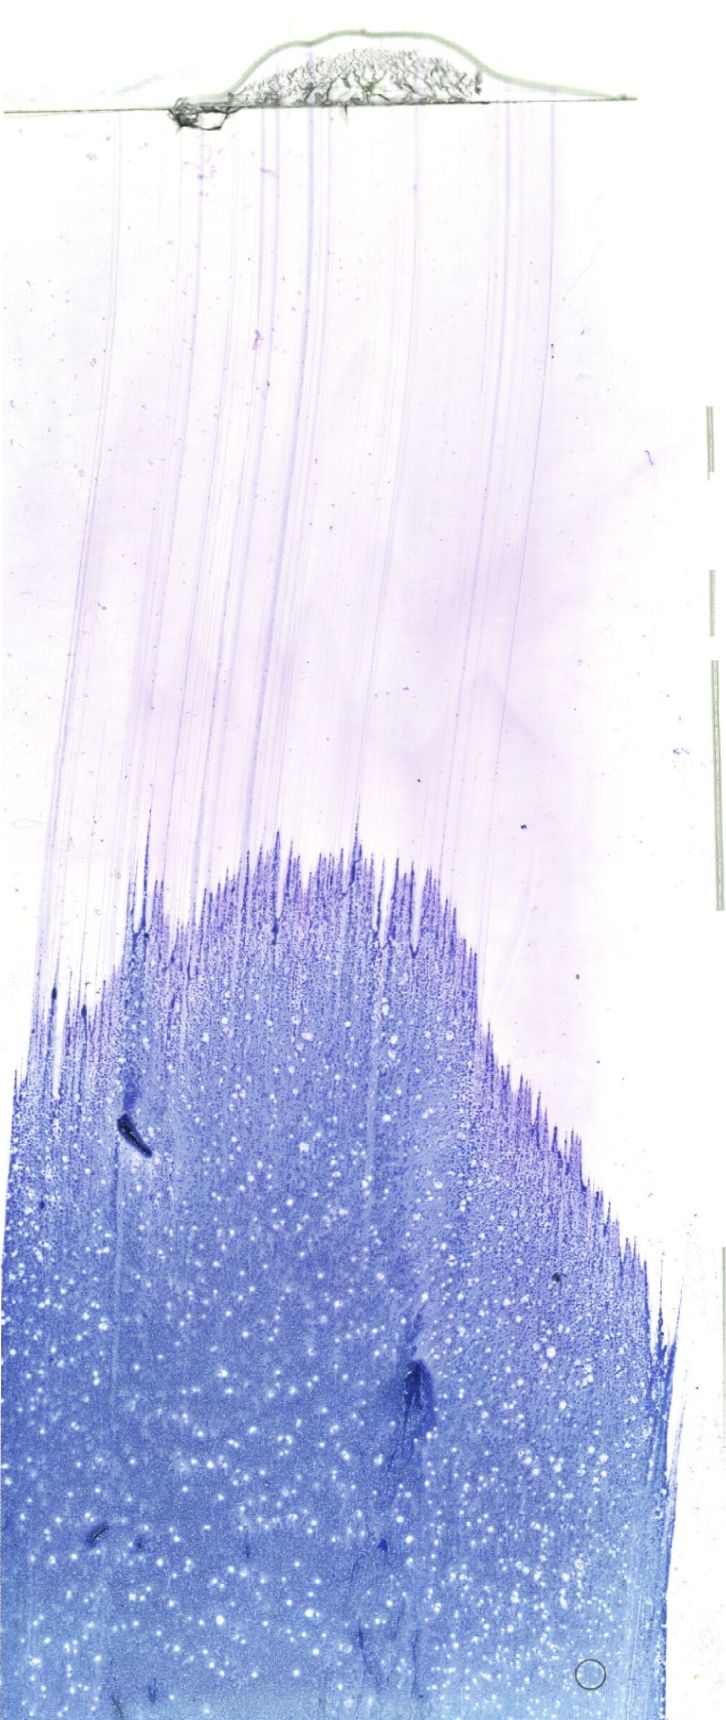
Whole-slide image of a May-Grünwald-Giemsa (MGG)-stained bone marrow aspirate smear — whole scanned area (about 20.6 x 48.8 mm) shown as a low-resolution overview. Patient sex: male.
Diagnosis: Acute Myeloid Leukemia without Maturation.